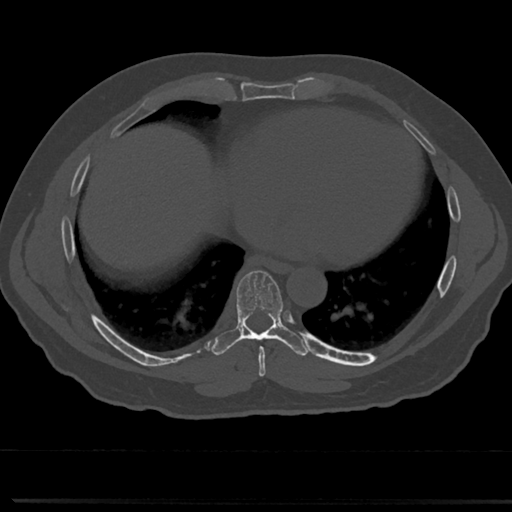
CT including the spine, one axial slice. Slice 364 of 817 in the series (ordered by position). Reconstruction kernel Br40s/3. Bone window (W 1800 / L 400 HU). 0.5 mm slice thickness. 512 × 512 image matrix. Male patient, age 61 years. Case-level facts recorded for this patient, not image findings: primary cancer: prostate.
Structures marked on this image (semi-automatic segmentation, software-assisted and operator-edited):
- T7 vertebra: bounding box <237,272,286,360> (left, top, right, bottom; pixels)
- T8 vertebra: <237,321,283,335>